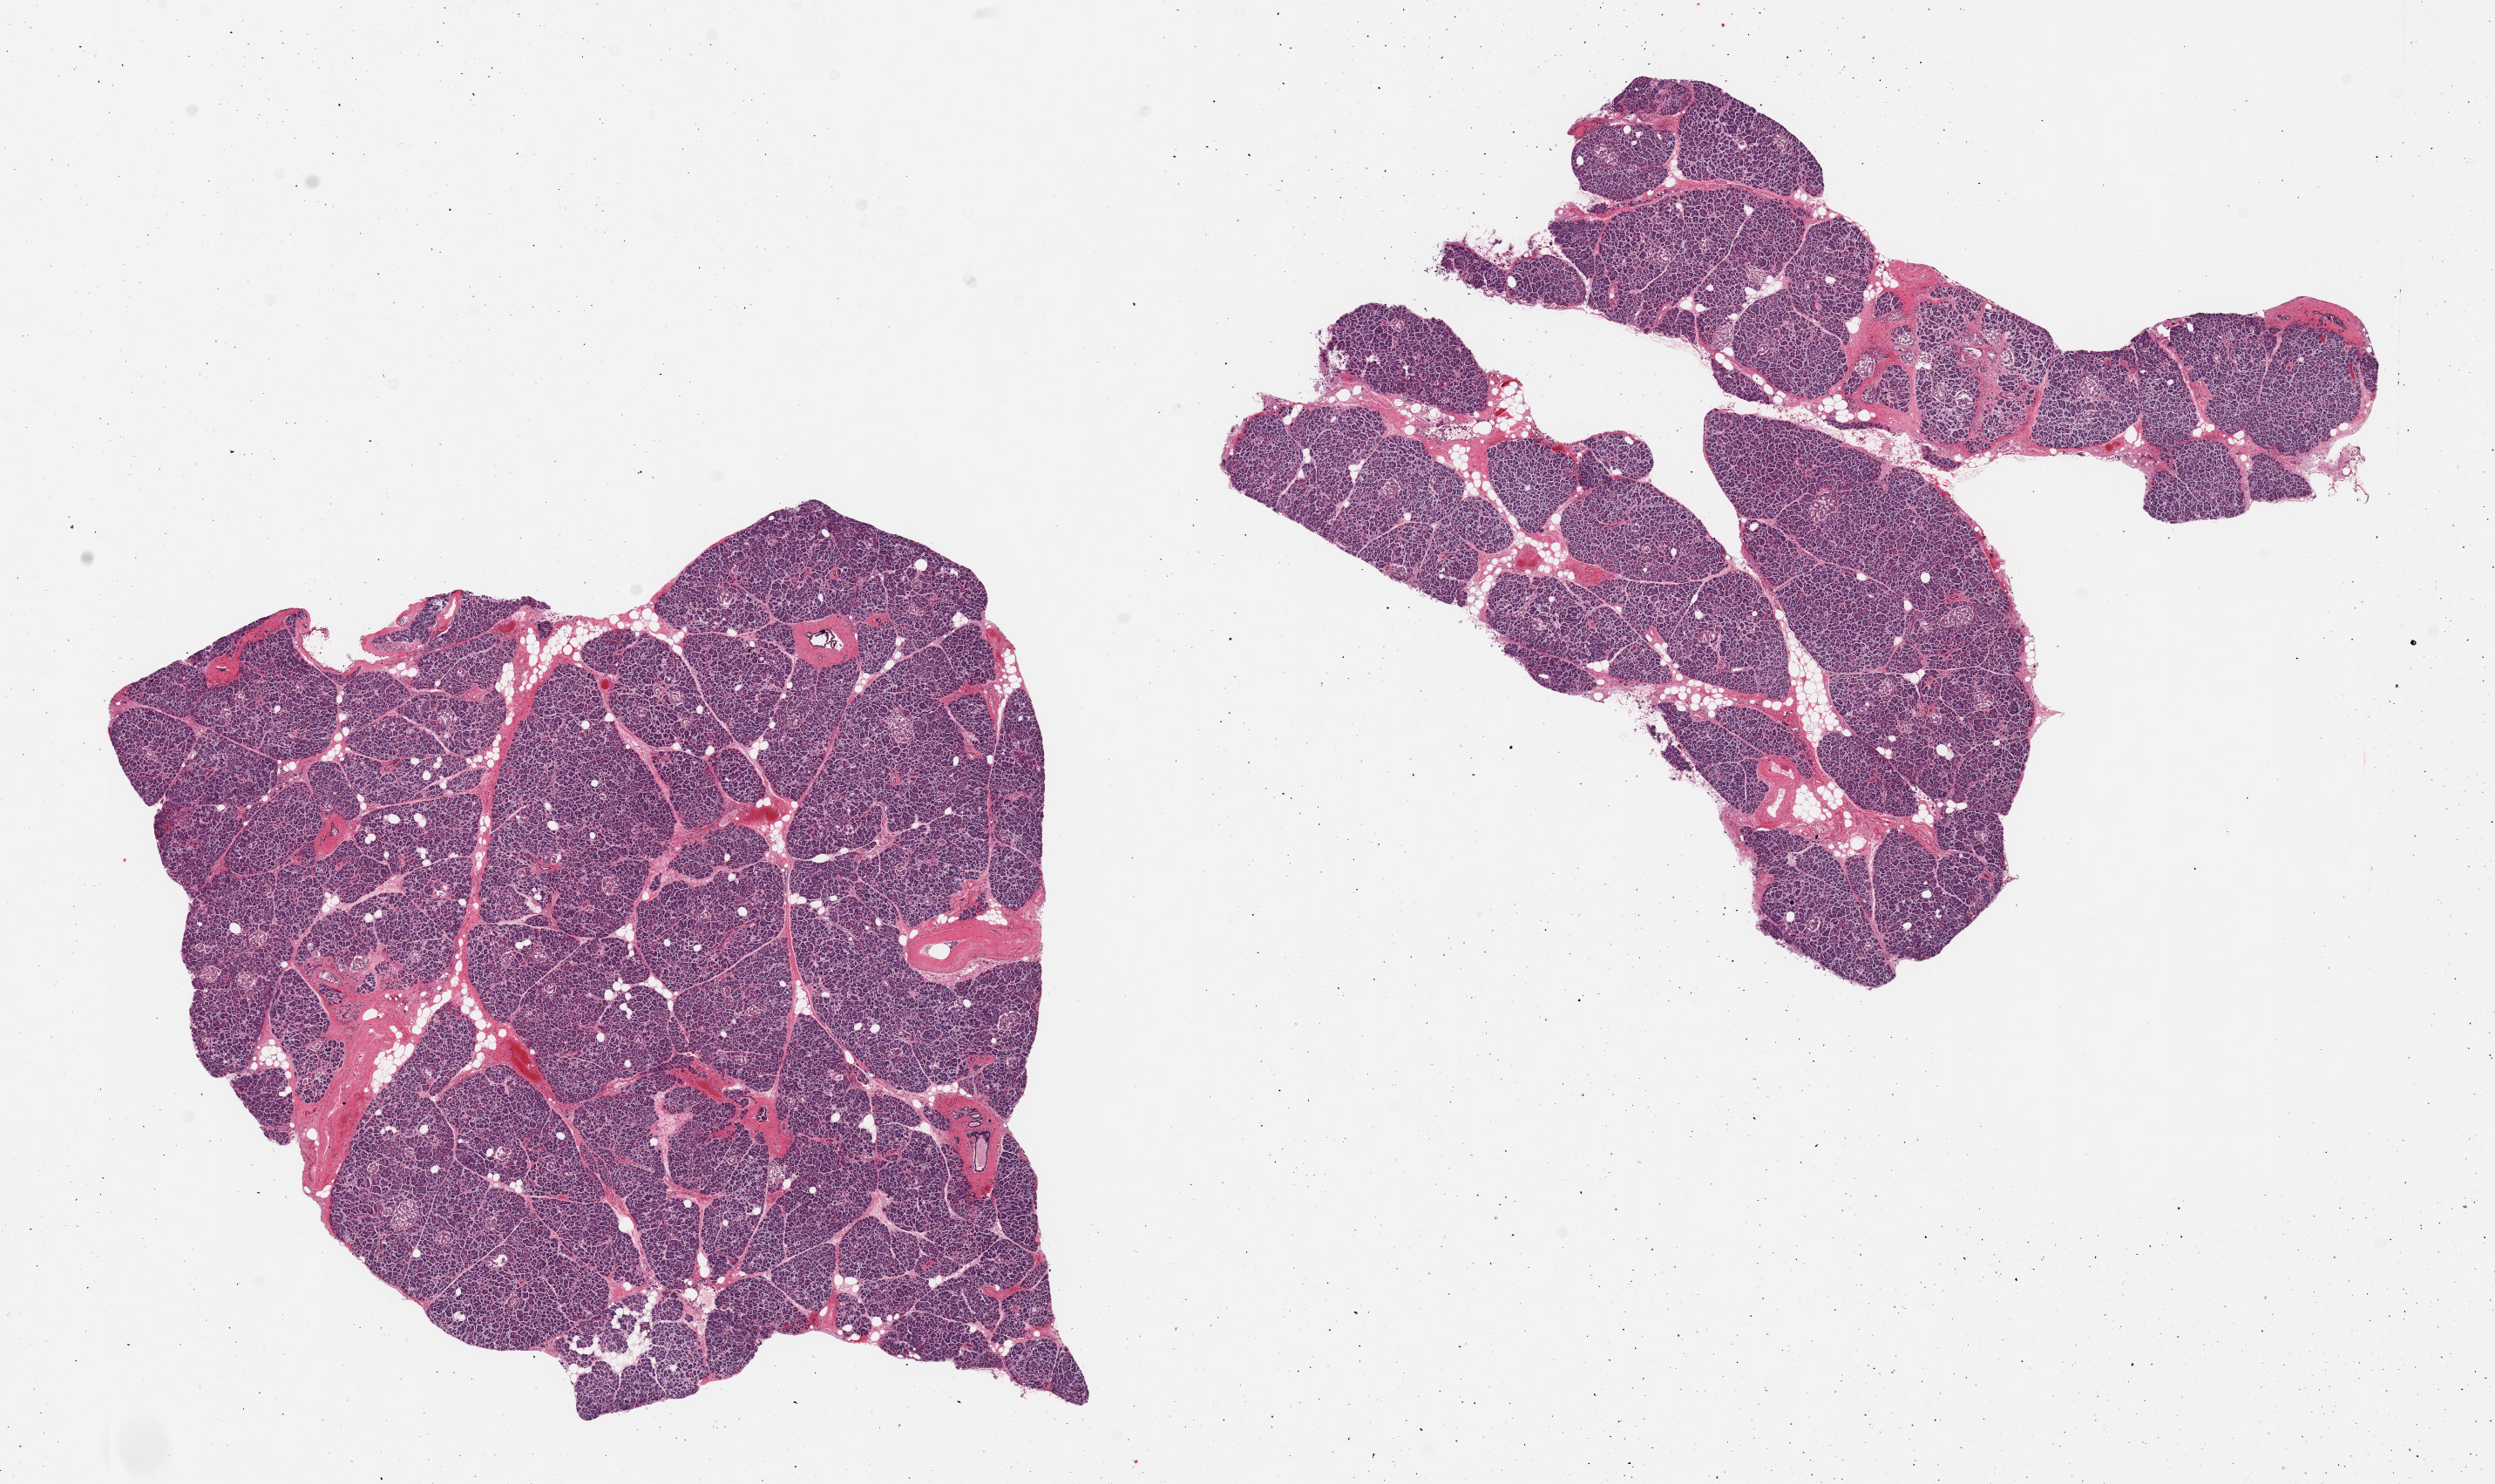
Whole-slide image, haematoxylin and eosin stain, shown as a low-resolution overview of the whole scanned area (about 22.6 x 13.5 mm, slide scanned at 20x); PAXgene-fixed paraffin-embedded (PFPE) section; section of pancreas (target tissue); tissue donor sample. Donor: female.
Reviewer comment on this tissue sample: 2 pieces; plentiful islets.